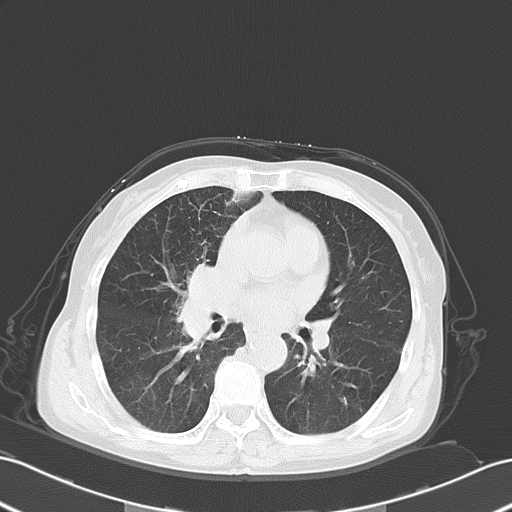
Chest CT, one axial slice; slice 28 of 55 in the series (ordered by position); reconstruction kernel B70f; lung window (W 1500 / L -600 HU); 512 × 512 image matrix, field of view 353 × 353 mm. Patient: female, 67 years. Case-level facts recorded for this patient, not image findings: clinical TNM (as recorded): T2a N3 M0; histopathological grade: G3.
Outlined on this slice (bounding box drawn by a radiologist):
- lung tumour (recorded histology: small cell carcinoma): bounding box [x1, y1, x2, y2] px = [173, 259, 223, 336]